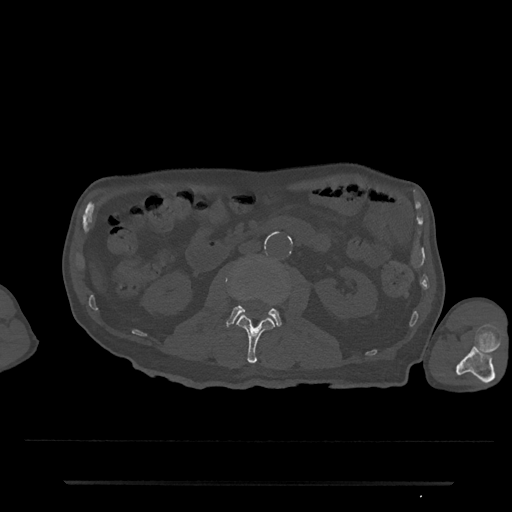
CT including the spine, one axial slice; position 29 of 797 along the scan axis; reconstruction kernel Br40s/3; 120 kVp; bone window (W 1800 / L 400 HU); 512 × 512 image matrix, field of view 427 × 427 mm. Patient: male, 74 years. Case-level facts recorded for this patient, not image findings: primary cancer: prostate.
Structures marked on this image (semi-automatically segmented with operator editing):
- L2 vertebra: bounding box (x1, y1, x2, y2) in pixels: (237, 300, 280, 364)
- L3 vertebra: (226, 305, 282, 328)